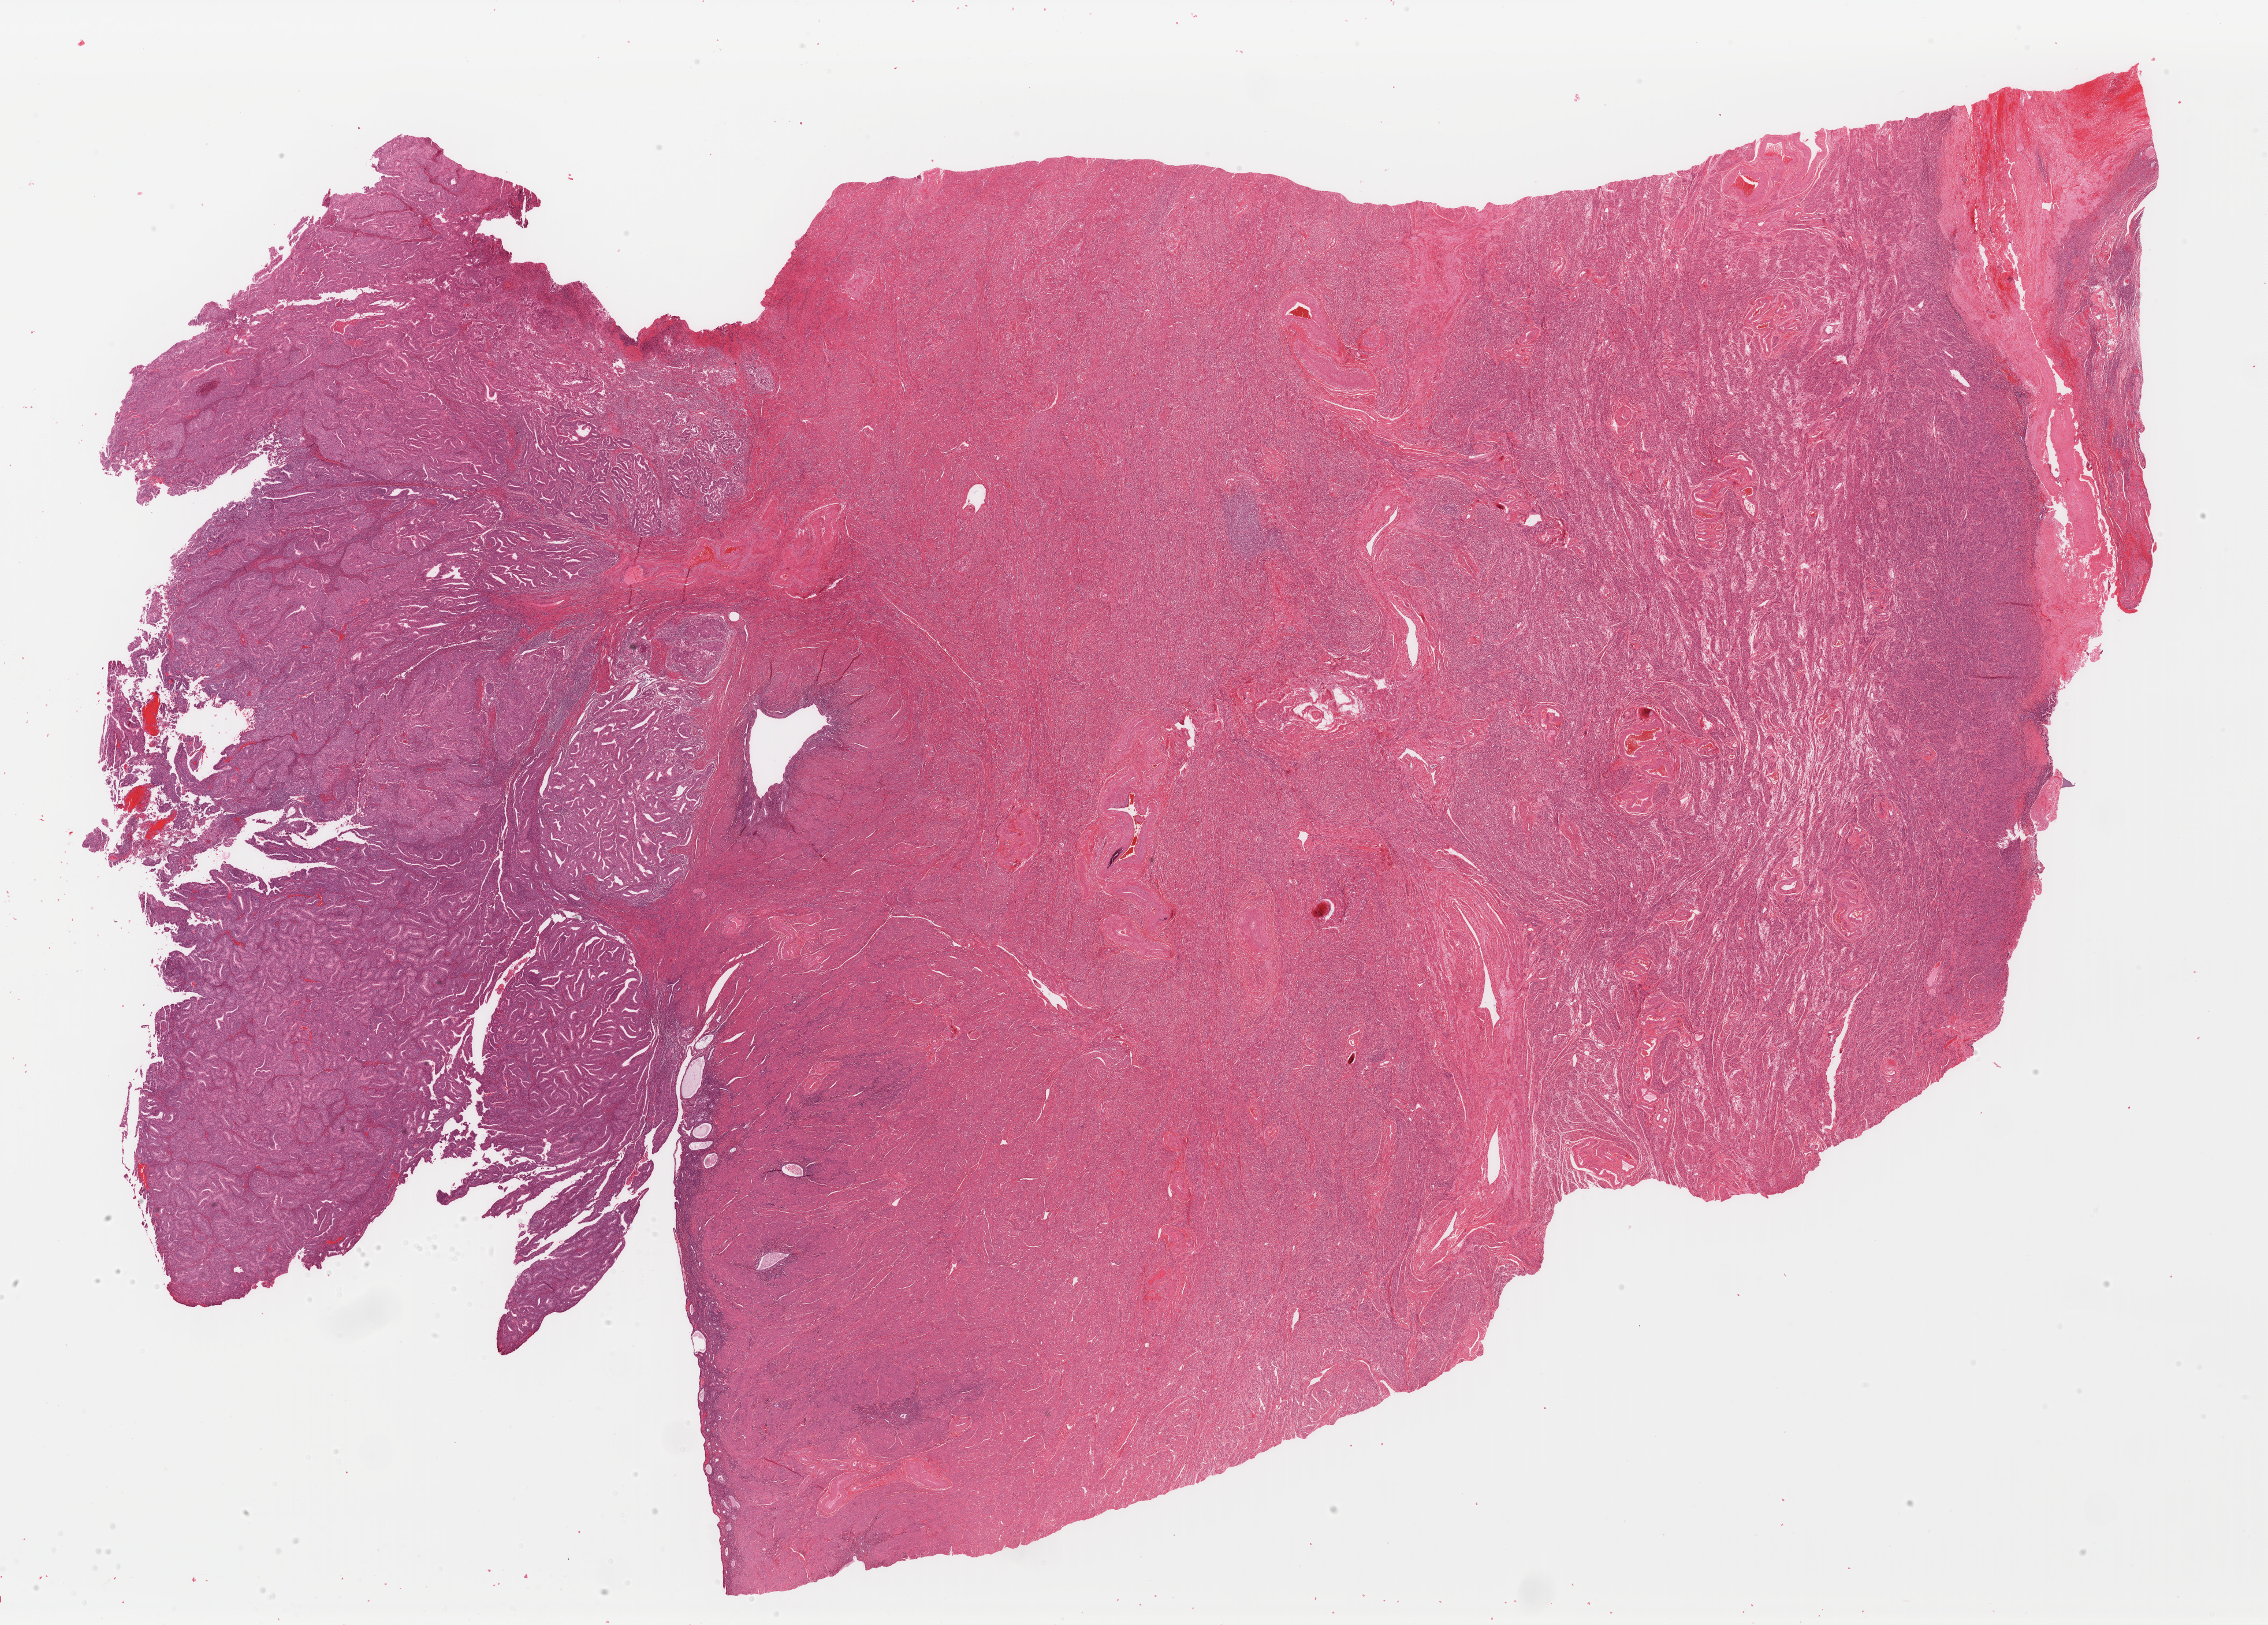
Digitized Hematoxylin and eosin (H&E) stained tissue section (whole slide), low-resolution overview of the scanned area, about 31.0 x 22.2 mm (from a 40x scan). Formalin-fixed paraffin-embedded (FFPE) diagnostic section. Sample: primary tumour, uterus. Female, age 63 years at initial diagnosis. Histologic grade: G2 (moderately differentiated).
- histologic diagnosis: Endometrioid adenocarcinoma, NOS (endometrium)
- FIGO stage: IB